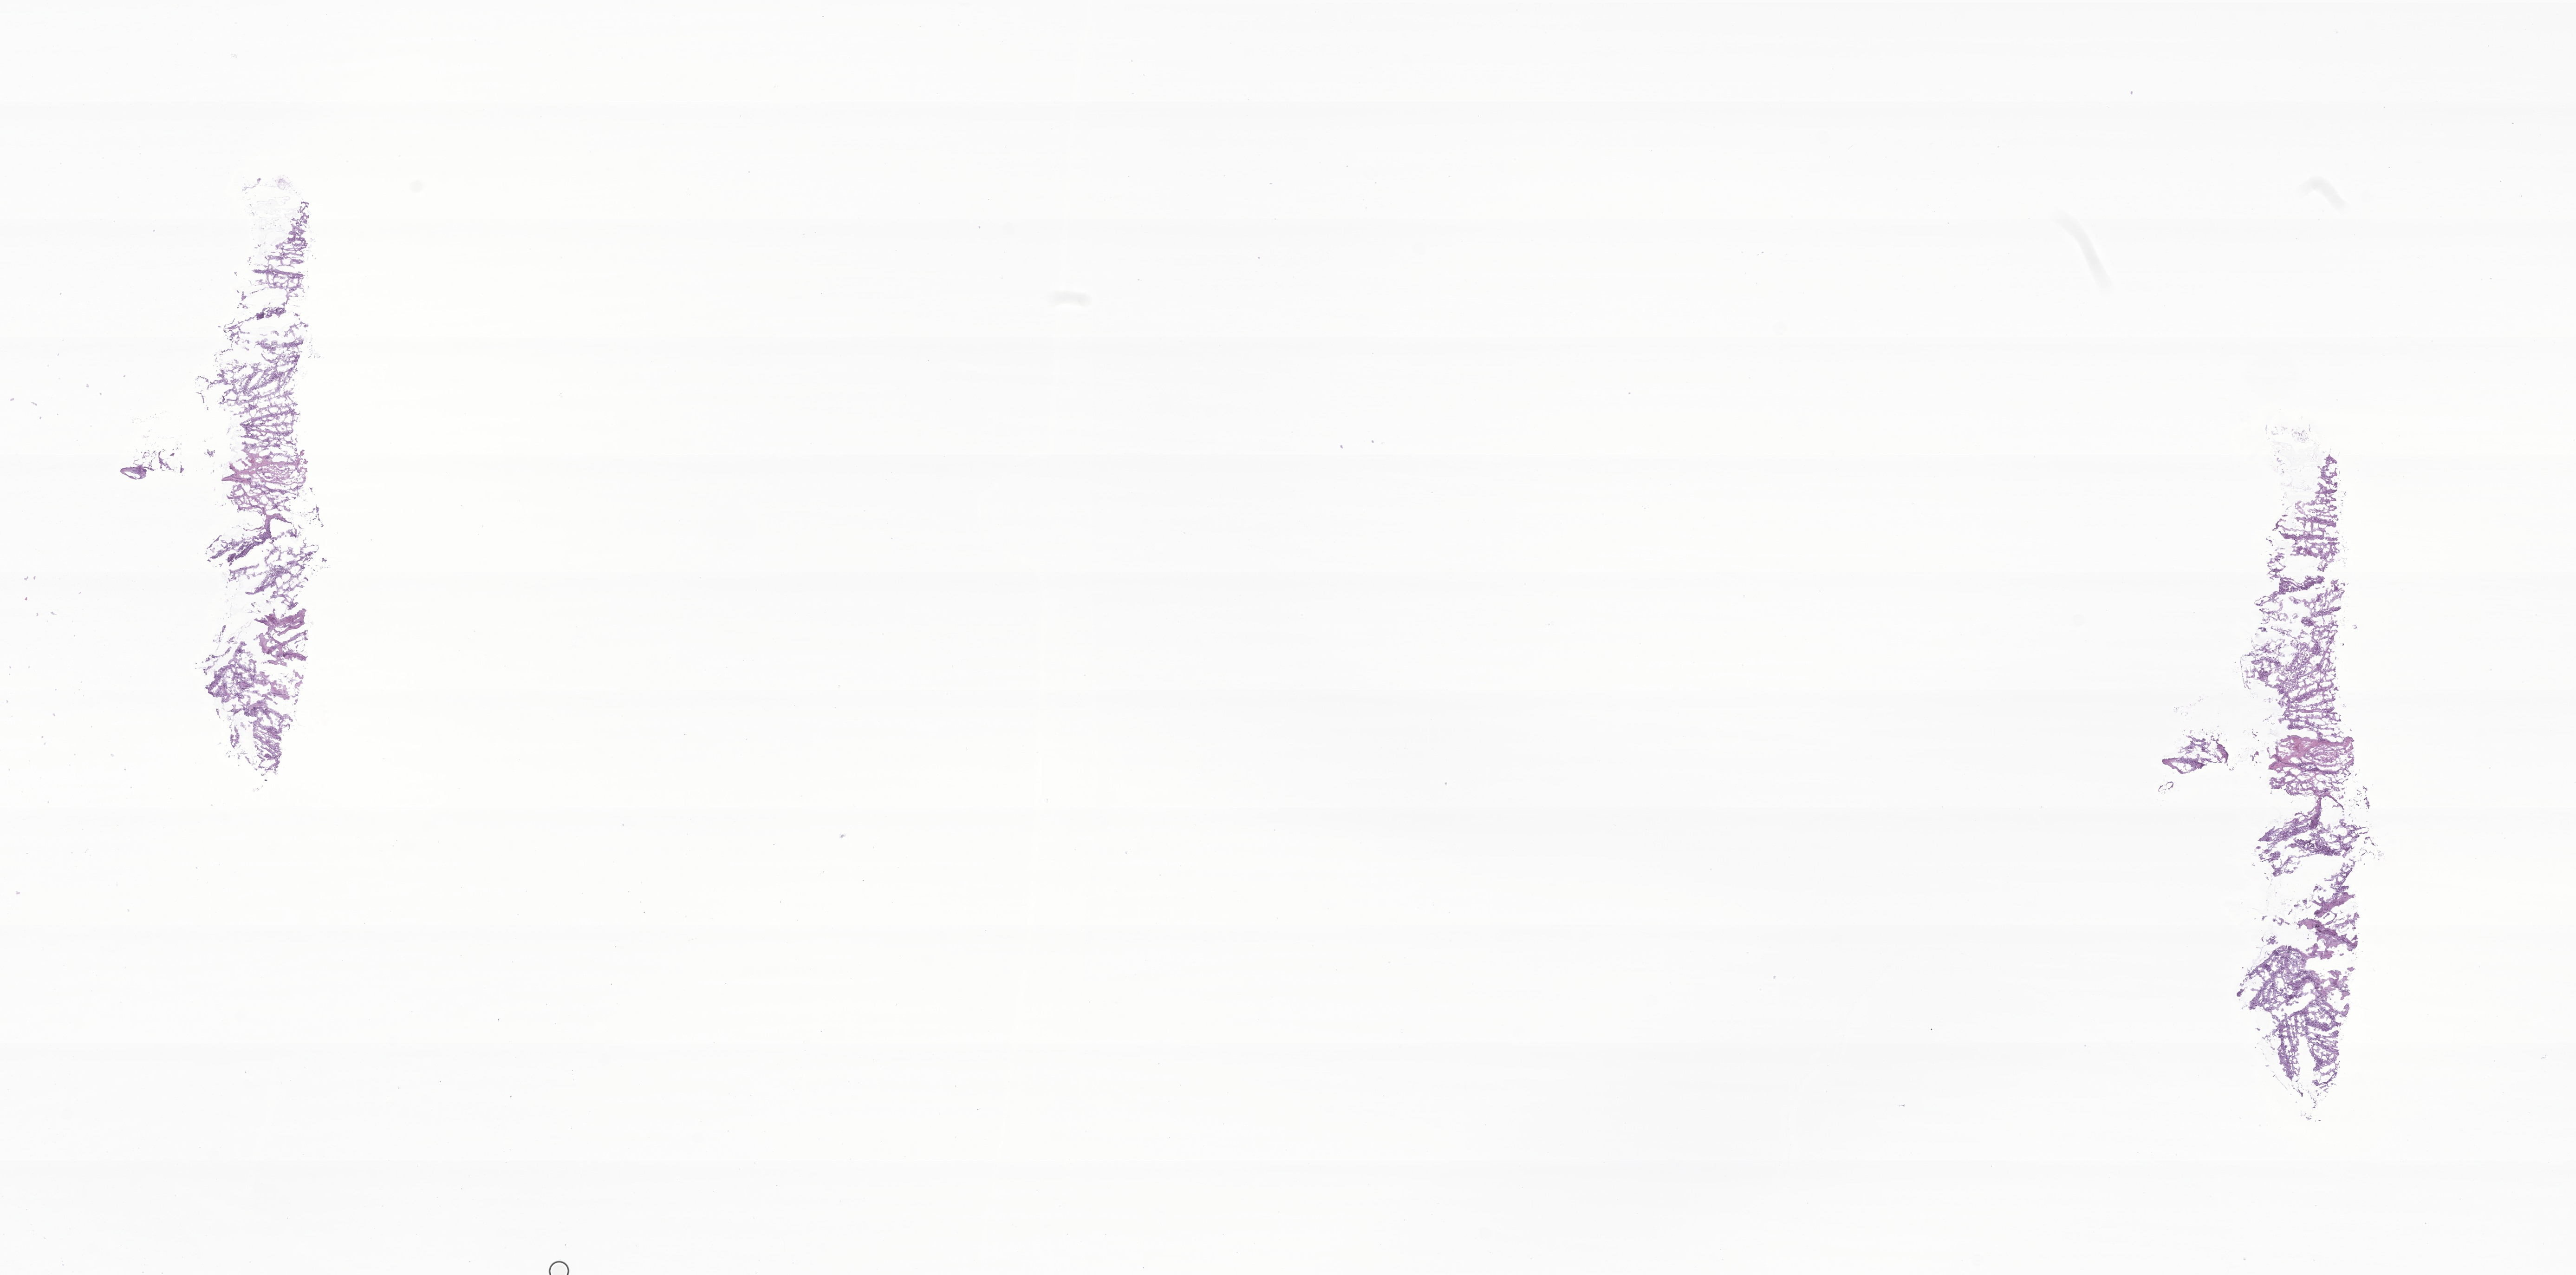
Whole-slide image, hematoxylin and eosin (H&E) stain of tumor tissue from the spinal cord, a low-resolution overview of the entire scanned area, about 23.4 x 11.6 mm; frozen section (OCT-embedded). Patient female; age 203 months.
Diagnosis: Myxopapillary ependymoma.